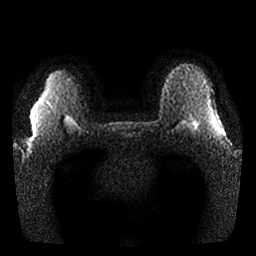
Breast MRI, one axial slice. Slice 23 of 25 in the series (ordered by position). Diffusion-weighted series; image 2 of 4 stored at this slice position (different b-values; order by instance number). 1.5 T. 4 mm slice thickness. 256 × 256 image matrix, field of view 340 × 340 mm. Female patient.
Structures marked on this image (outlined manually by an expert reader):
- tumour on diffusion-weighted imaging: bounding box <188,121,196,128> (left, top, right, bottom; pixels)